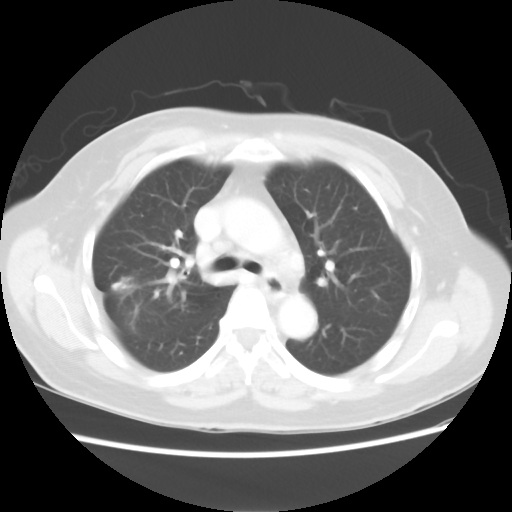
Chest CT, one axial slice; position 49 of 80 along the scan axis; reconstruction kernel STANDARD; lung window (W 1500 / L -600 HU); 5 mm slice thickness; 512 × 512 image matrix. Patient: female, 67 years. Case-level facts recorded for this patient, not image findings: clinical TNM (as recorded): T1c N1 M0.
Outlined on this slice (rectangle marked by the reading radiologist):
- lung tumour (recorded histology: adenocarcinoma): bounding box (x1, y1, x2, y2) in pixels: (108, 268, 145, 306)